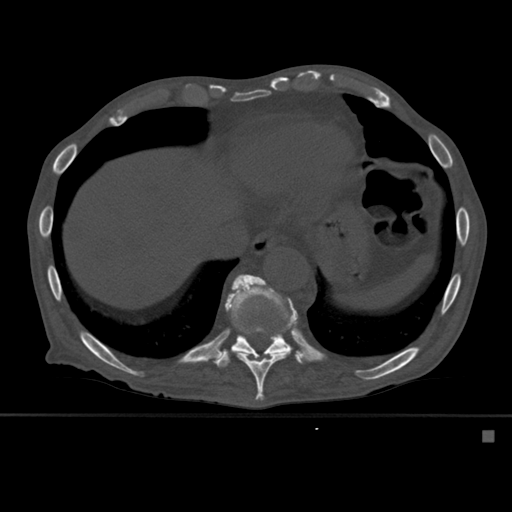
CT including the spine, one axial slice. Bone window (W 1800 / L 400 HU). 1.5 mm slice thickness. 512 × 512 image matrix, field of view 373 × 373 mm. Male patient, age 78 years. Case-level facts recorded for this patient, not image findings: primary cancer: prostate.
Structures marked on this image (semi-automatic segmentation, software-assisted and operator-edited):
- T10 vertebra: box from (x=225, y=274) to (x=298, y=401) px
- T11 vertebra: (x=214, y=299)–(x=304, y=368)